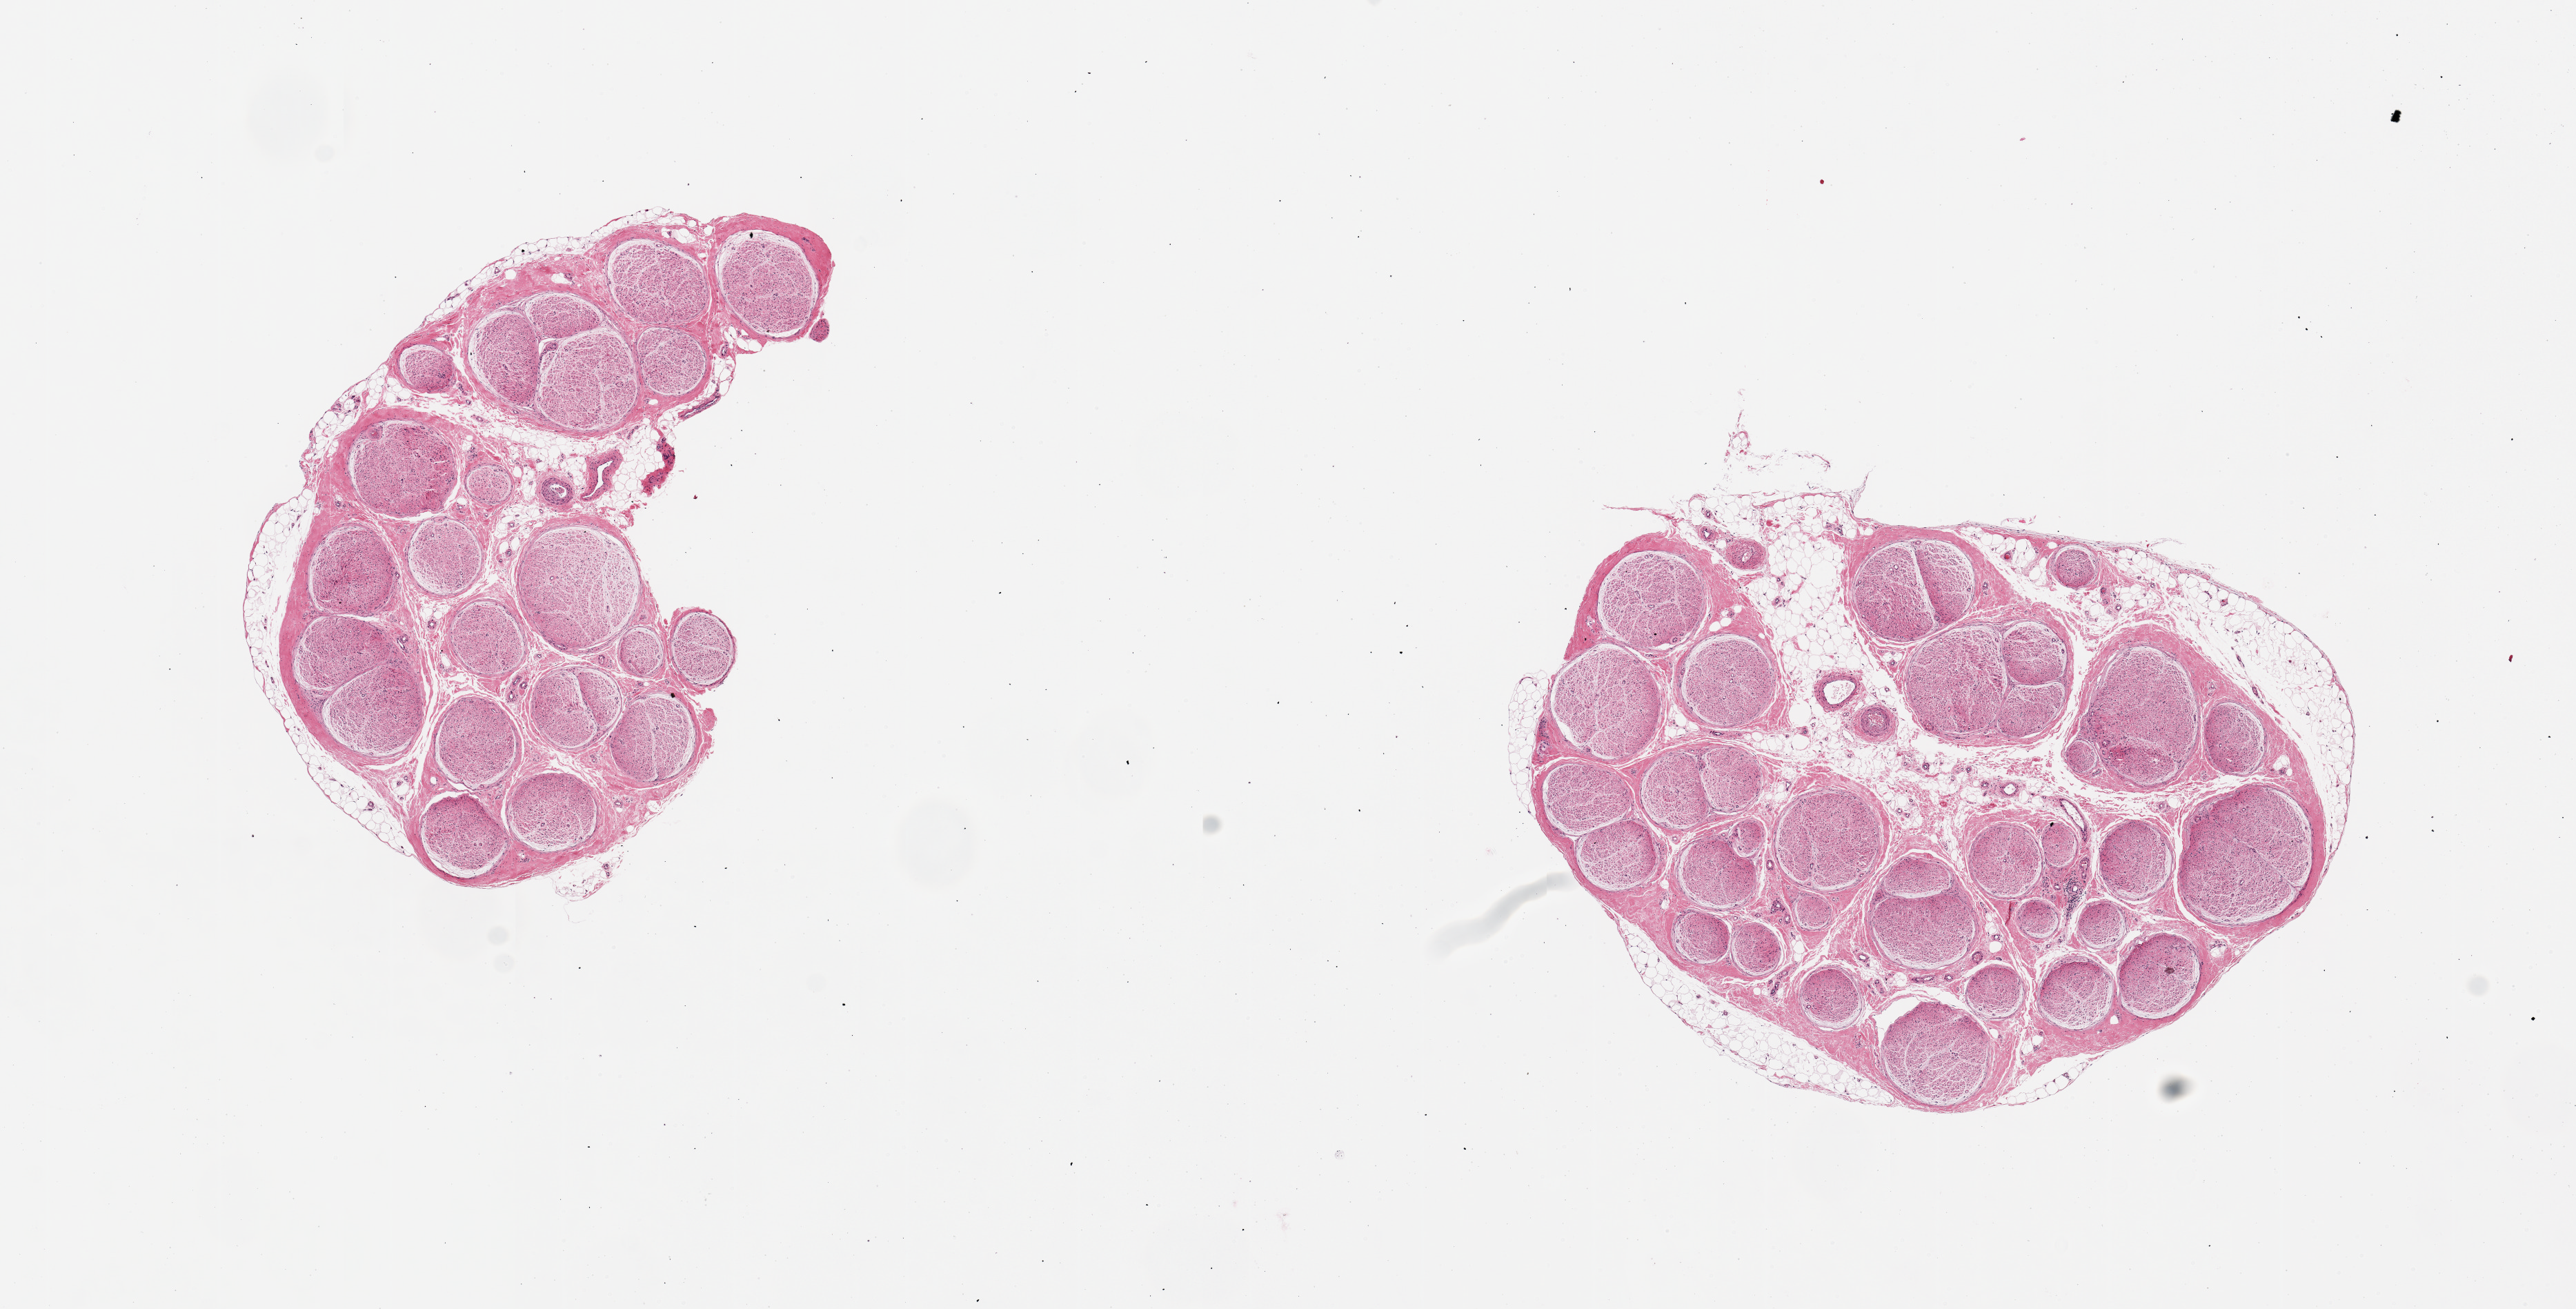
H&E whole-slide image, low-resolution overview of the scanned area, about 14.8 x 7.5 mm (acquisition: 20x scan); PAXgene-fixed paraffin-embedded (PFPE) section; section of tibial nerve (target tissue); donor tissue sample. Donor: female.
Review note (as recorded): 2 pieces, 4x3 & 5x3mm; 10 & 20% internal and external adipose.